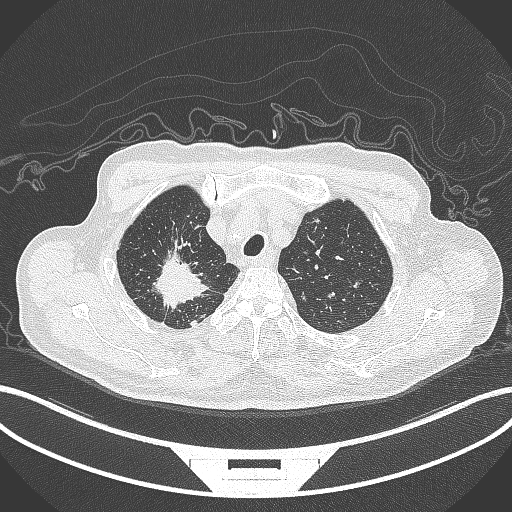
Chest CT, one axial slice; slice 322 of 407 in the series (ordered by position); reconstruction kernel B70f; 120 kVp; lung window (W 1500 / L -600 HU); 1 mm slice thickness; 512 × 512 image matrix. Patient: male, 69 years. From the clinical record (not read from this slice): clinical TNM (as recorded): T1c N1 M1.
Outlined on this slice (bounding box drawn by a radiologist):
- lung tumour (recorded histology: adenocarcinoma): bounding box <144,247,218,314> (left, top, right, bottom; pixels)